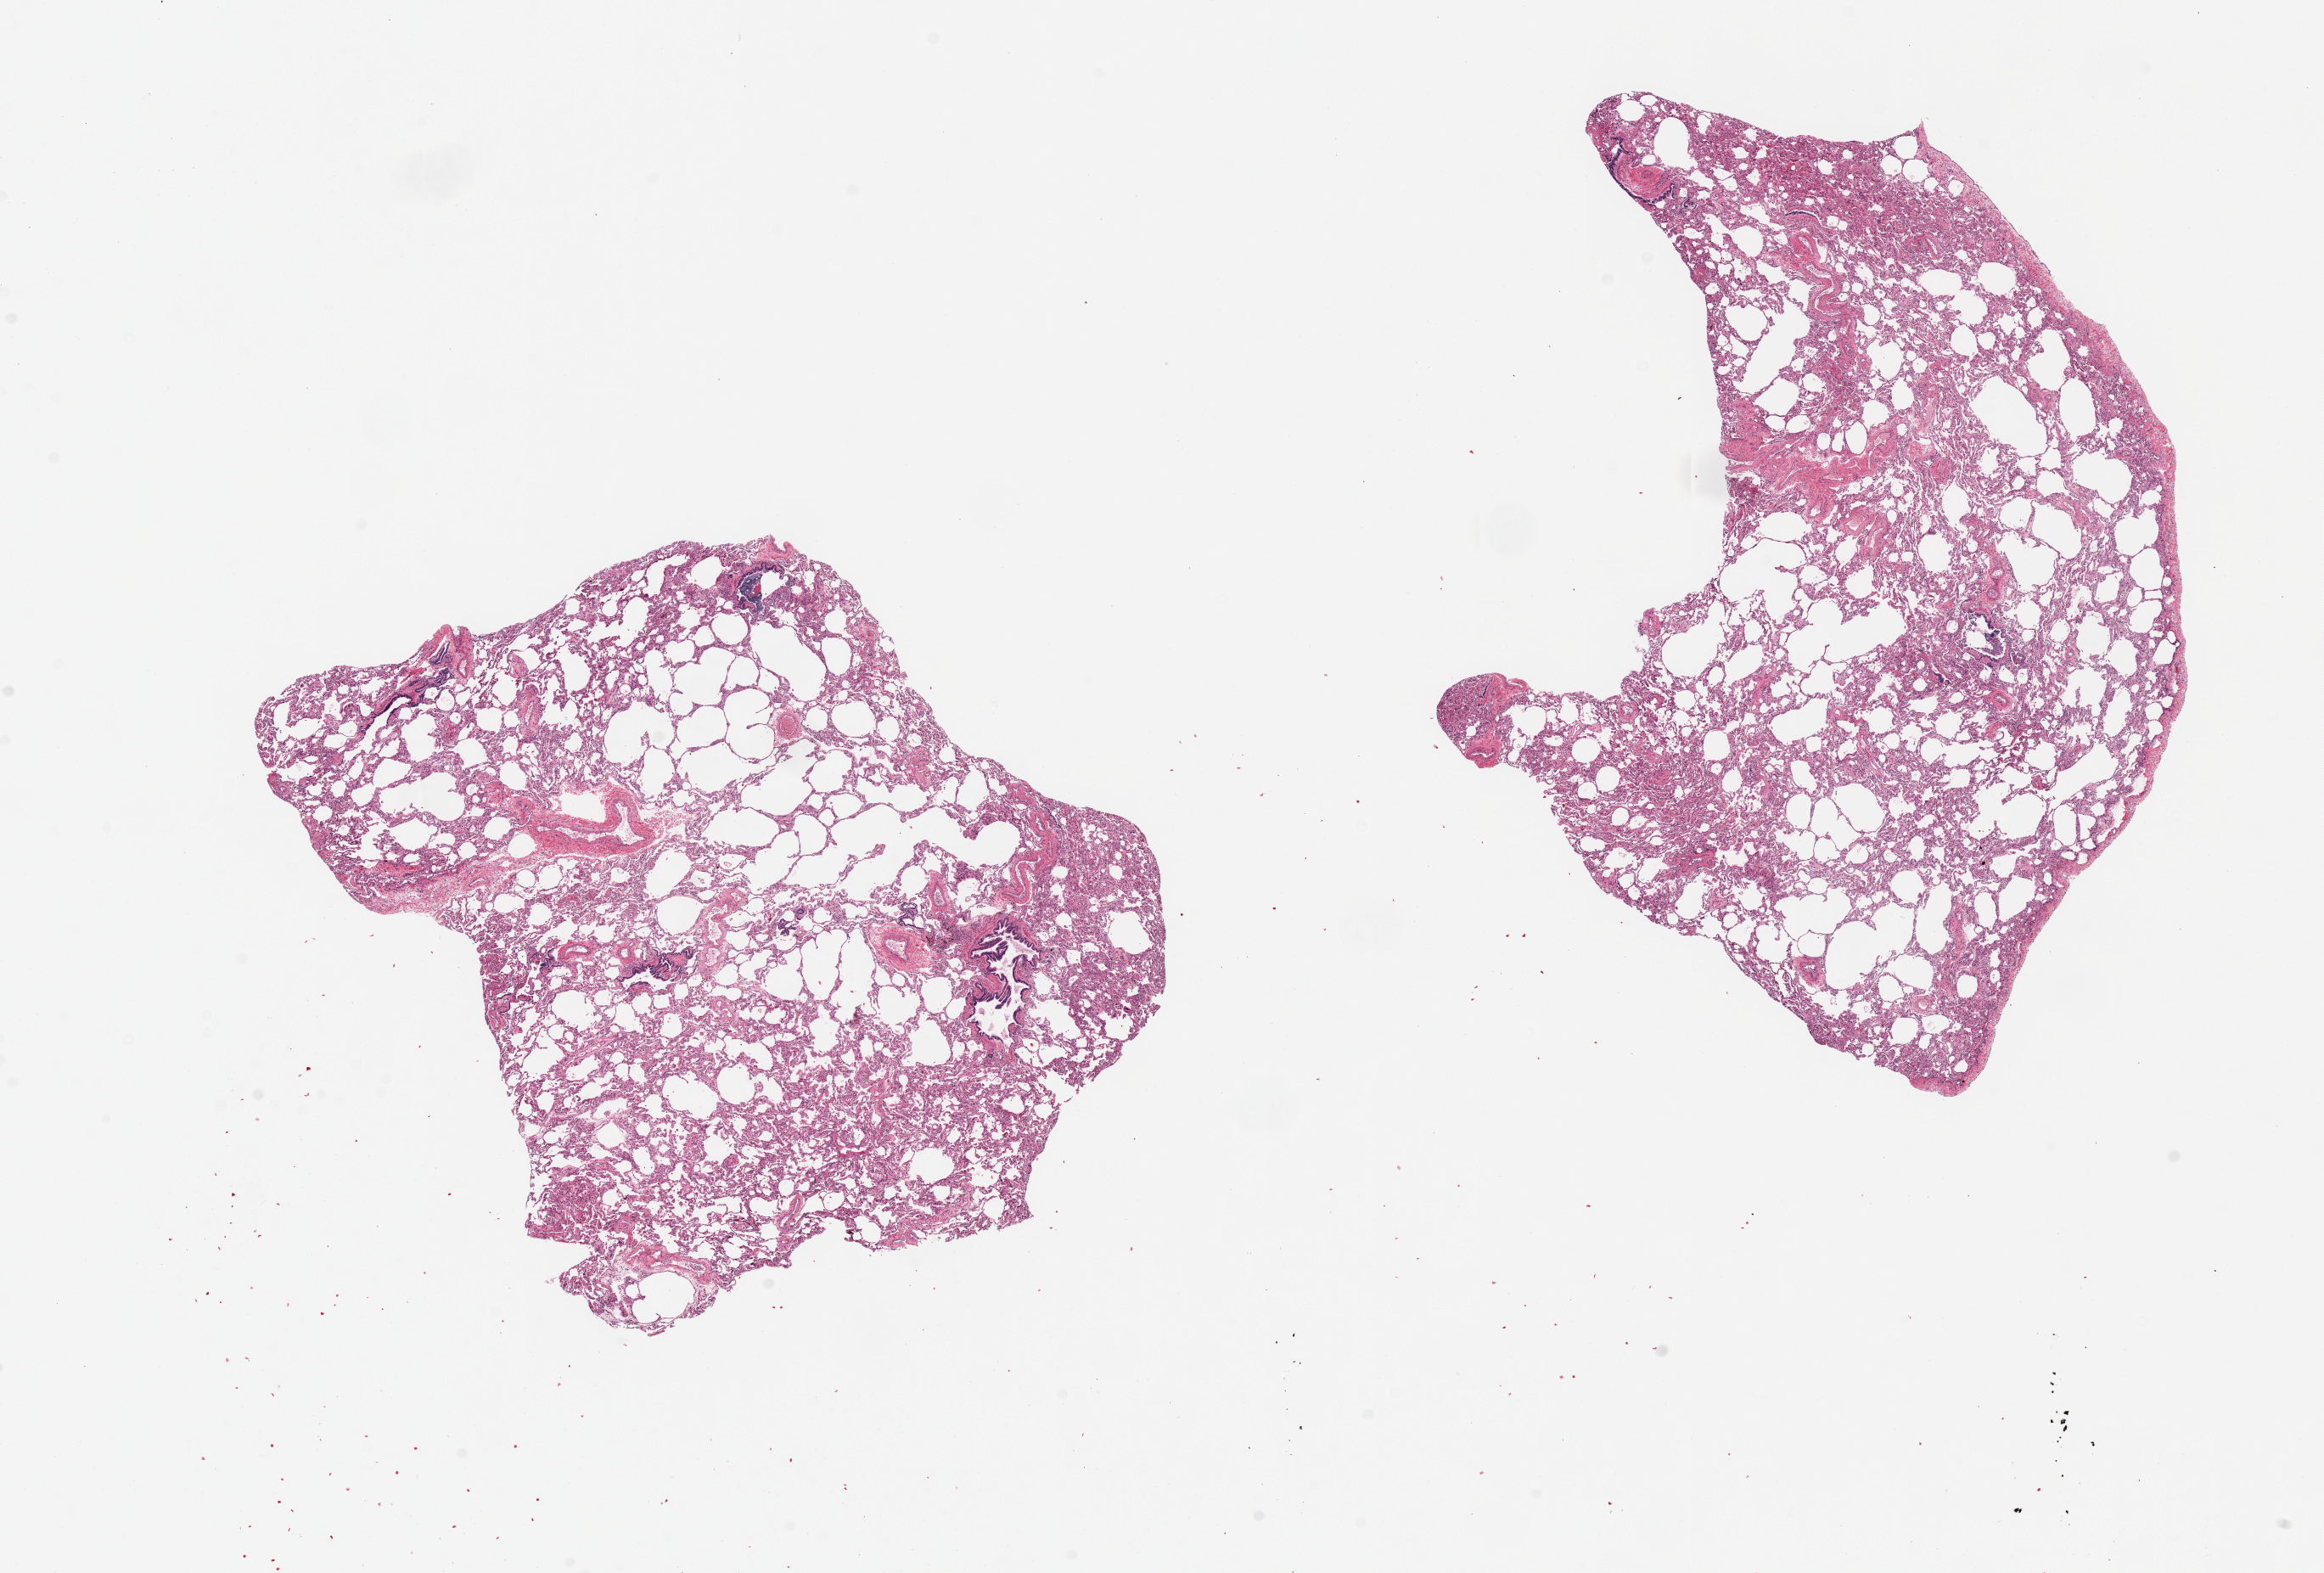
Whole-slide image, H&E stain, brightfield, a low-resolution overview of the entire scanned area, about 21.7 x 14.7 mm; PAXgene-fixed, paraffin-embedded tissue; section of lung (target tissue); donor tissue sample. Male donor.
- pathologist's review note for this sample: 2 pieces, 8x7 & 10x6mm; patchy emphysematous changes, bronchiolar metaplasia noted